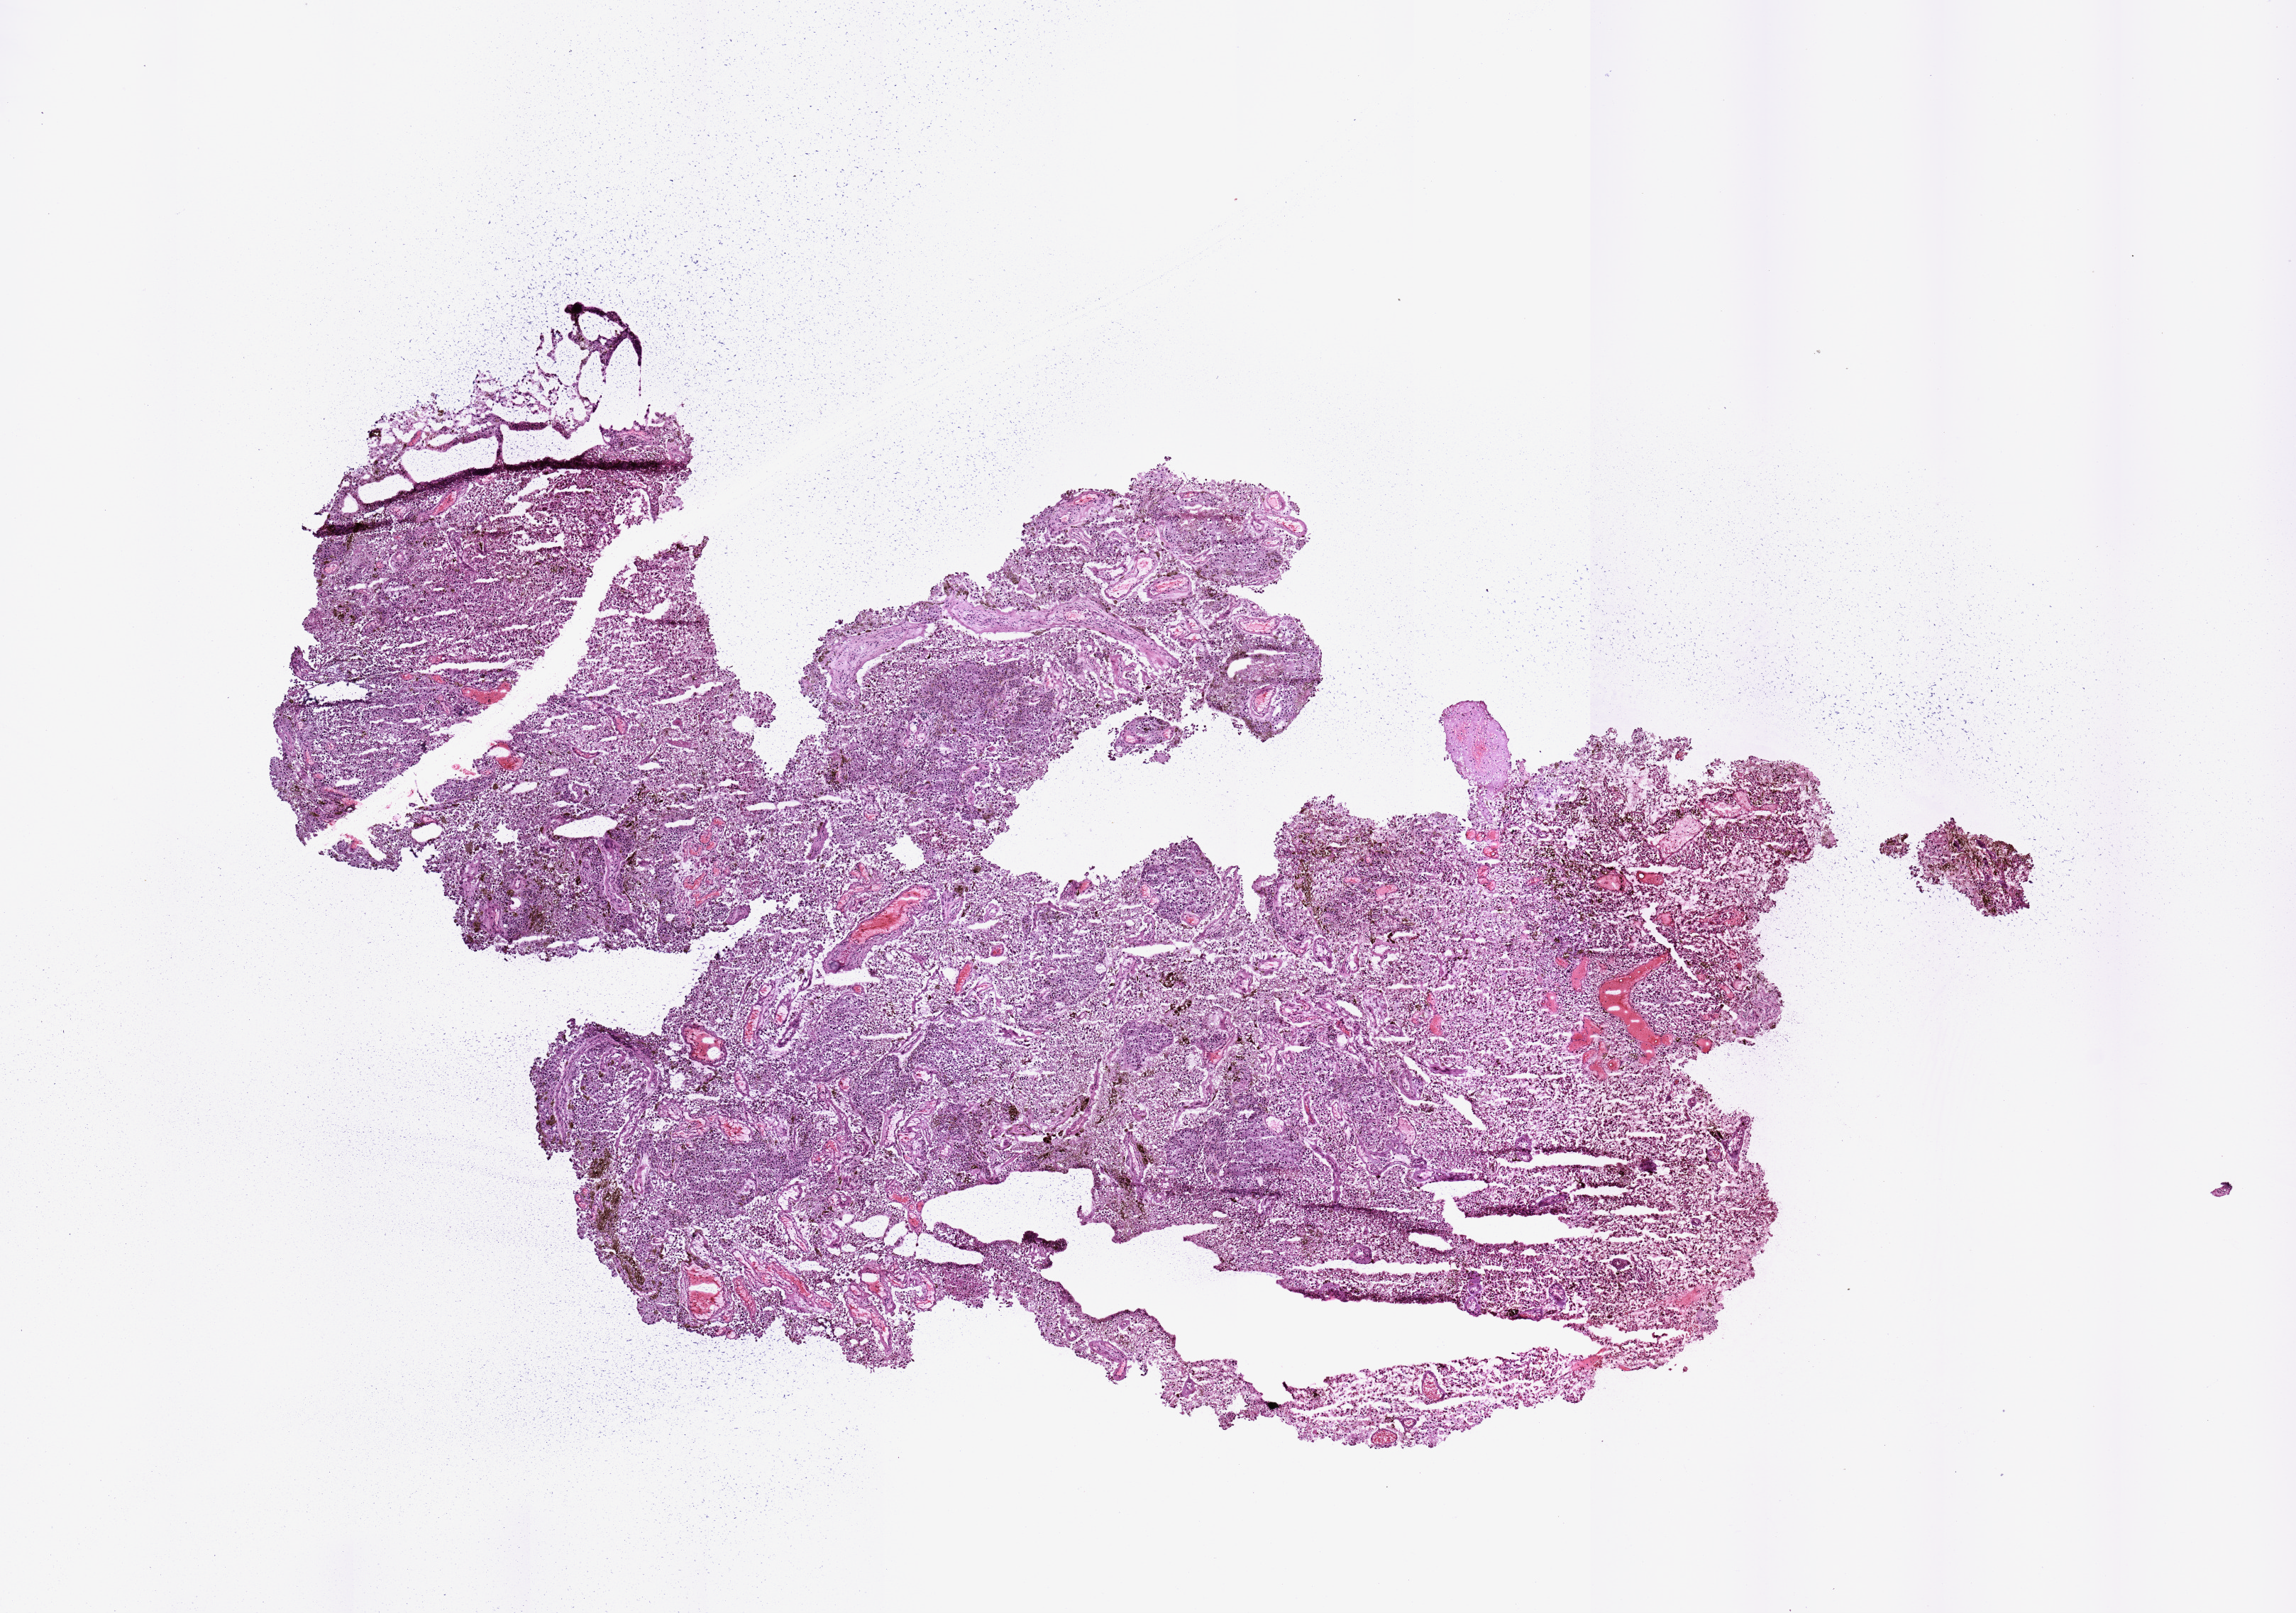
Hematoxylin and eosin (H&E) stained whole-slide image — a low-resolution overview of the entire scanned area, about 12.8 x 9.0 mm (slide scanned at 20x), melanoma tumour tissue; sampled site not recorded. Patient: male, age 75 years.
- patient diagnosis (cohort enrolment): cutaneous melanoma (skin)
- primary tumour site (as recorded): head & neck